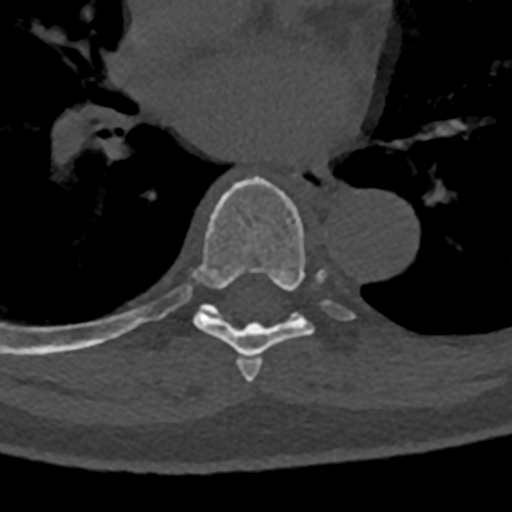
CT including the spine, one axial slice. Slice 756 of 797 in the series (ordered by position). Bone window (W 1800 / L 400 HU). 0.5 mm slice thickness. 512 × 512 image matrix, field of view 160 × 160 mm. Patient: male, 74 years. From the clinical record (not read from this slice): primary cancer: renal; vertebrae with lytic lesions (as recorded): T10, L1, L2, L3, L4, L5.
Structures marked on this image (semi-automatic segmentation, software-assisted and operator-edited):
- T6 vertebra: bounding box (x1, y1, x2, y2) in pixels: (242, 358, 263, 383)
- T7 vertebra: (71, 176, 355, 371)
- T8 vertebra: (70, 321, 141, 351)